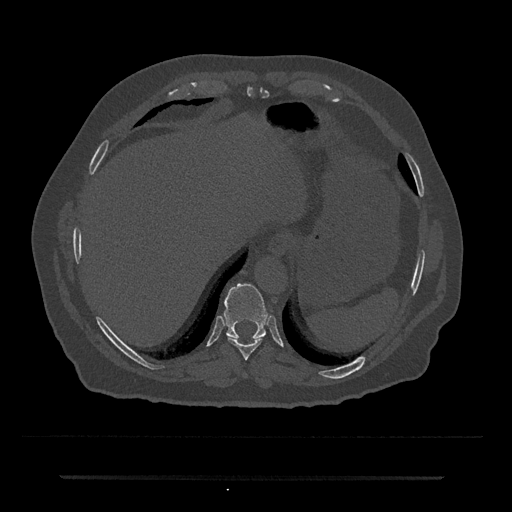
CT including the spine, one axial slice. Slice 255 of 797 in the series (ordered by position). 120 kVp. Bone window (W 1800 / L 400 HU). 0.5 mm slice thickness. 512 × 512 image matrix, field of view 437 × 437 mm. Patient: male, 69 years. From the clinical record (not read from this slice): primary cancer: prostate.
Outlined on this slice (semi-automatically segmented with operator editing):
- T10 vertebra: bounding box <224,283,267,340> (left, top, right, bottom; pixels)
- T9 vertebra: <227,336,262,360>